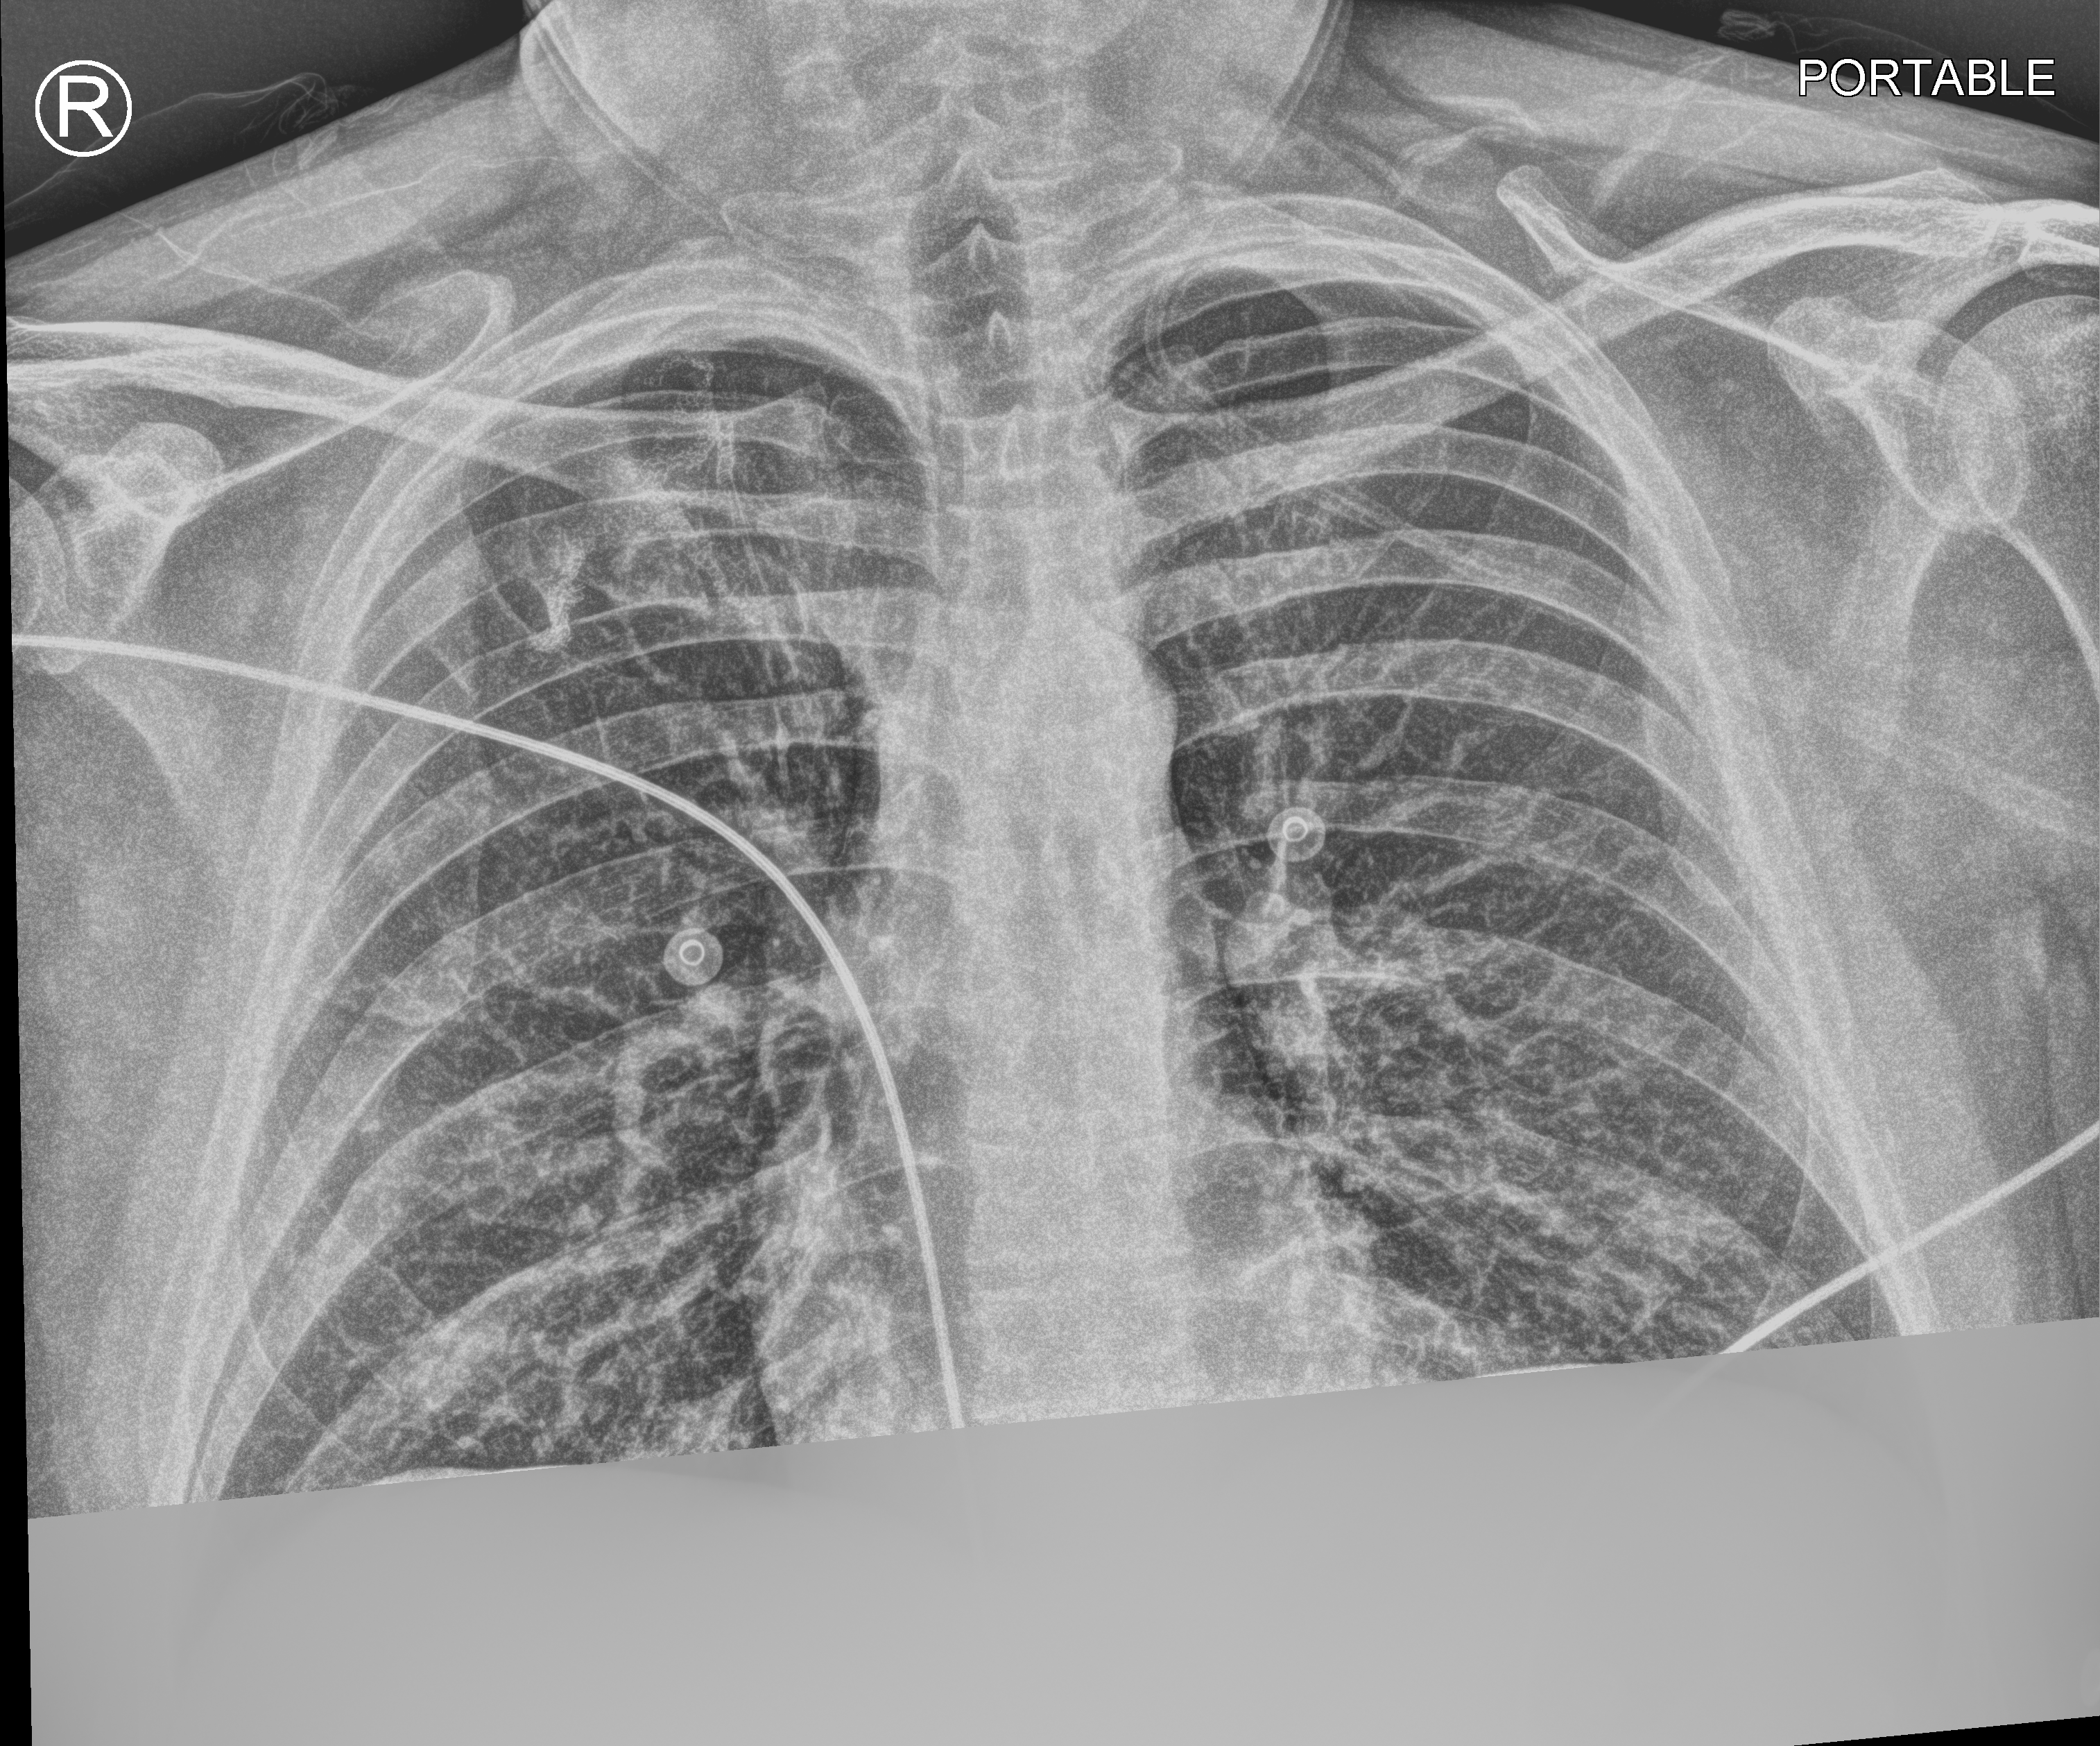
Portable chest radiograph, anteroposterior (AP) projection. Male patient hospitalised with COVID-19, age 18–59 years.
From the hospital-stay record, not from the radiograph (when in the stay this image was taken is not recorded): length of hospital stay: 1 day; mechanically ventilated during this hospital stay: no.